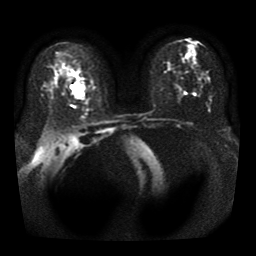
Breast MRI, one axial slice. Position 21 of 41 along the scan axis. Diffusion-weighted series; image 2 of 4 stored at this slice position (different b-values; order by instance number). 1.5 T. 5 mm slice thickness. 256 × 256 image matrix, field of view 330 × 330 mm. Female patient.
Structures marked on this image (outlined manually by an expert reader):
- tumour on diffusion-weighted imaging: bounding box [x1, y1, x2, y2] px = [69, 82, 84, 98]